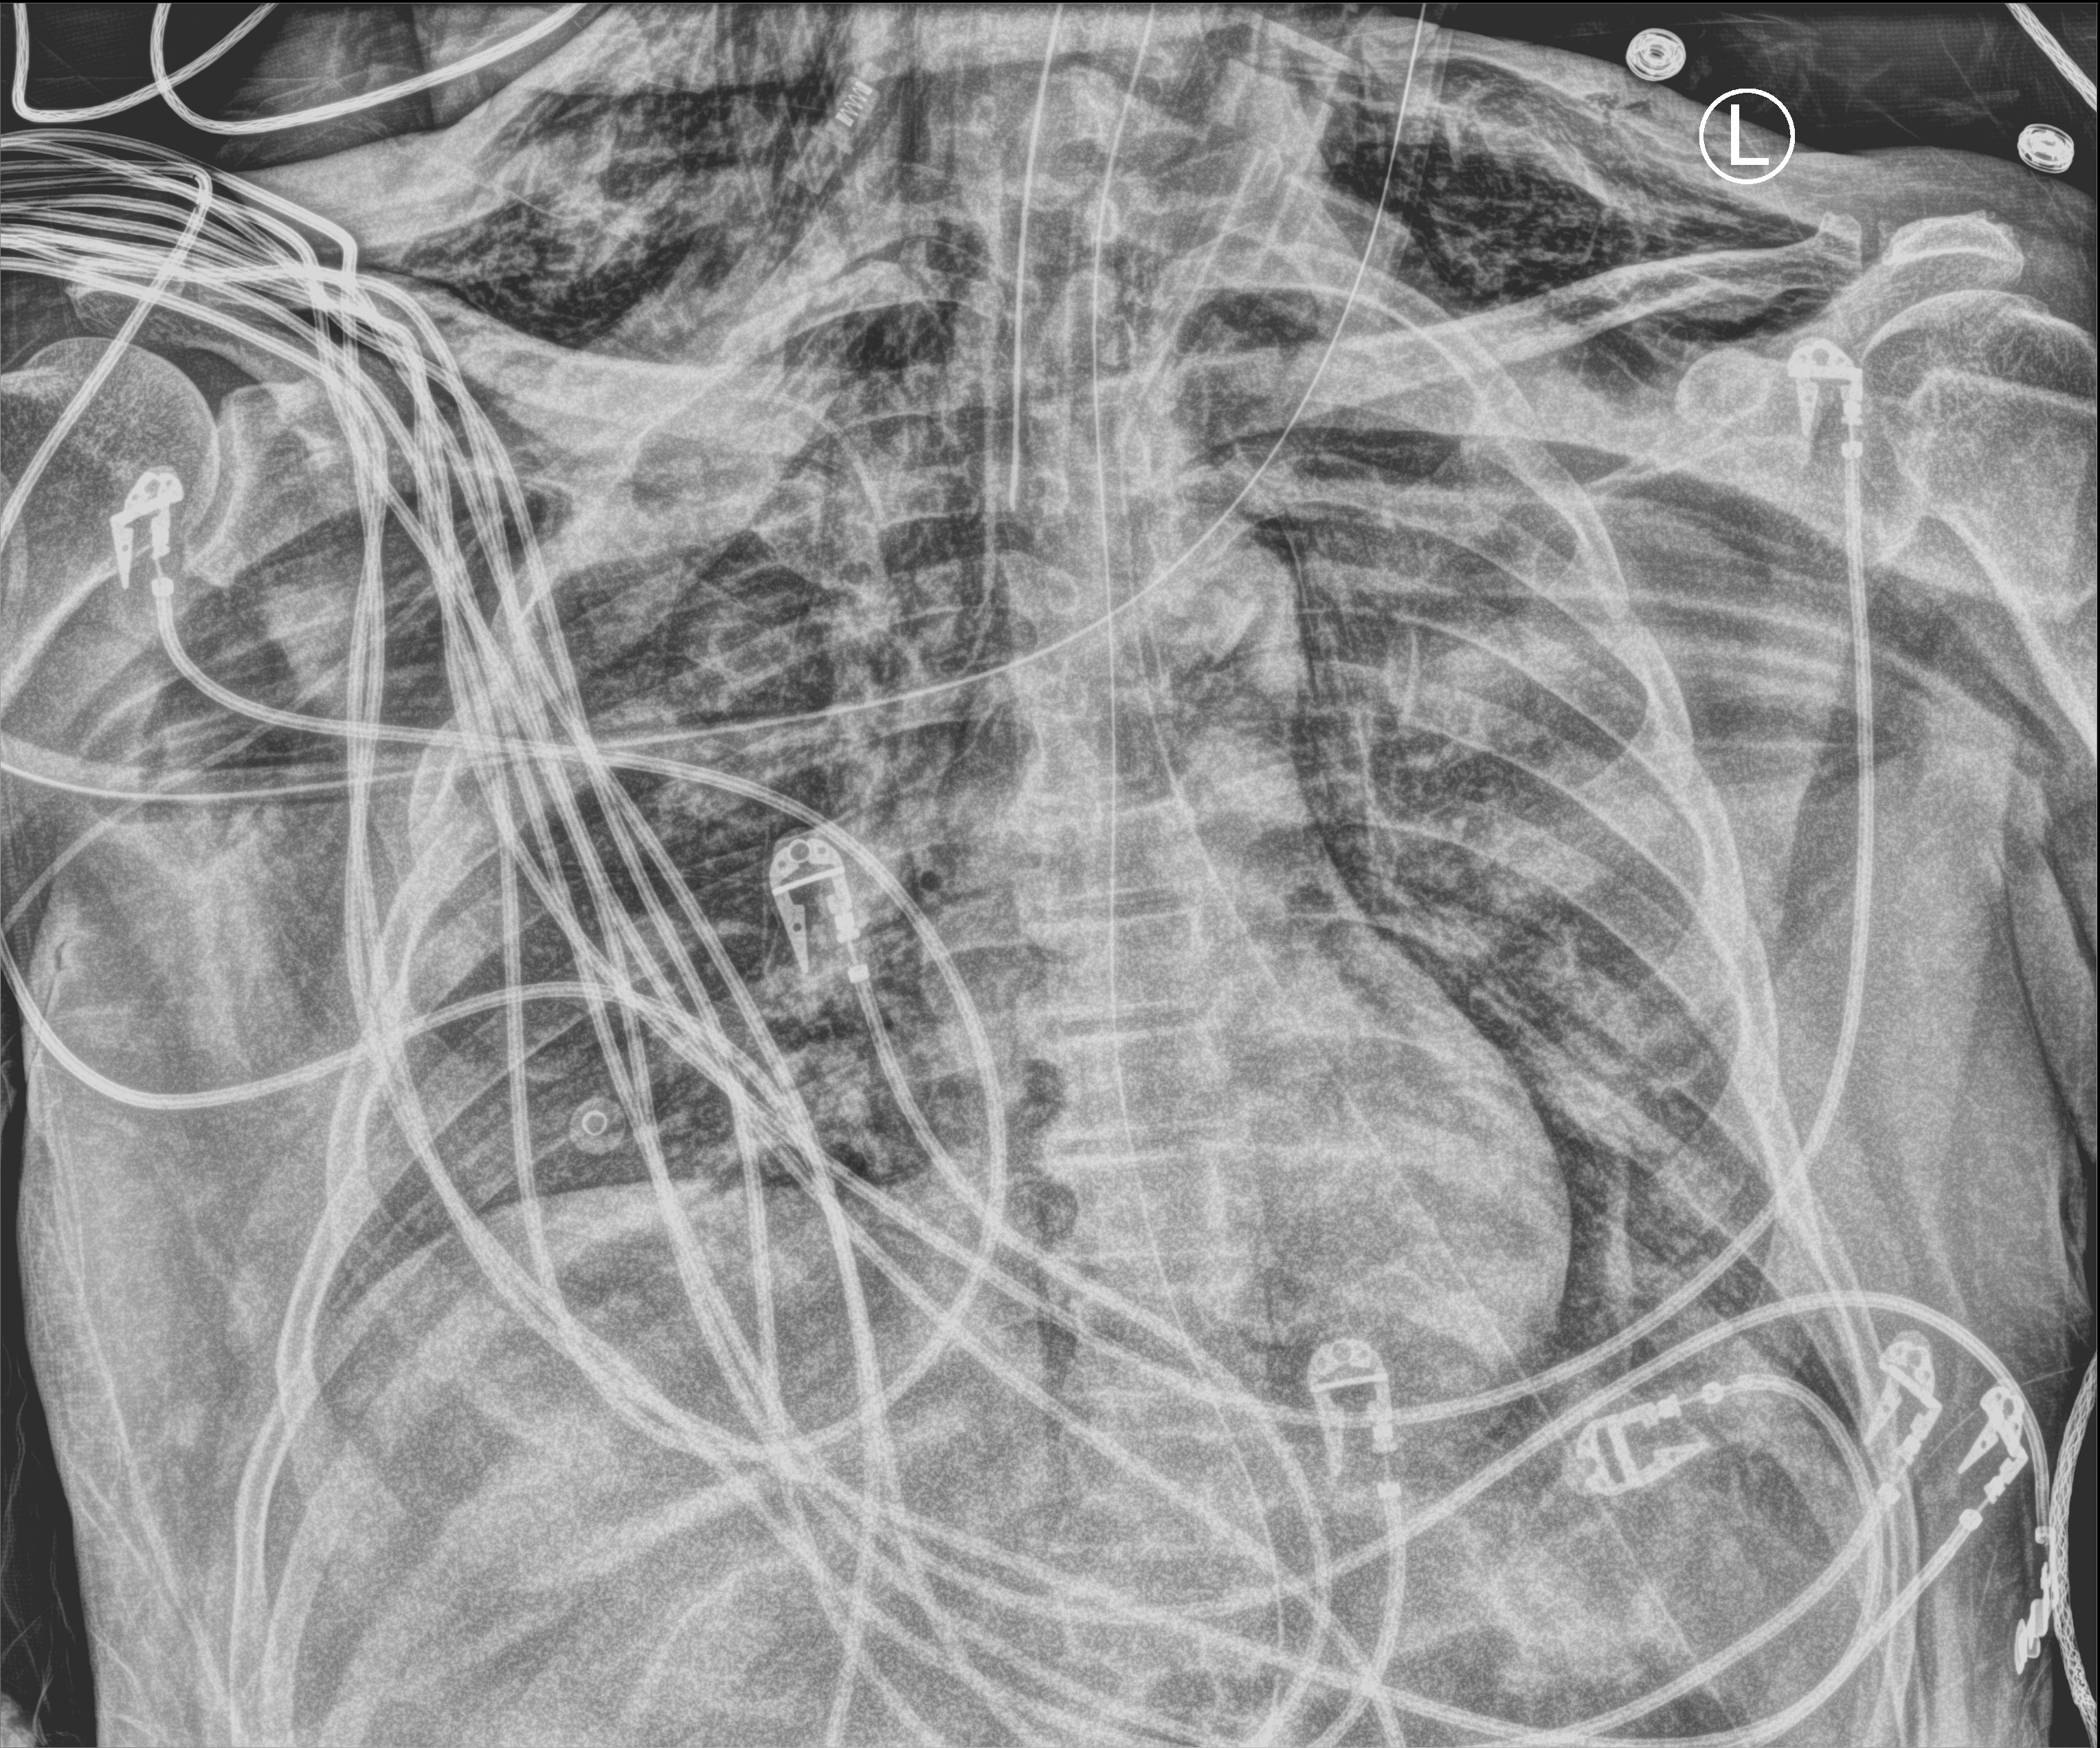
Portable chest radiograph; anteroposterior (AP) projection. Male patient hospitalised with COVID-19, age 18–59 years.
Admission-level facts for this patient (not findings on this image; timing relative to this image not recorded):
- admitted to intensive care during this hospital stay: yes
- chronic kidney disease (admission record): no
- smoking status (admission record): never